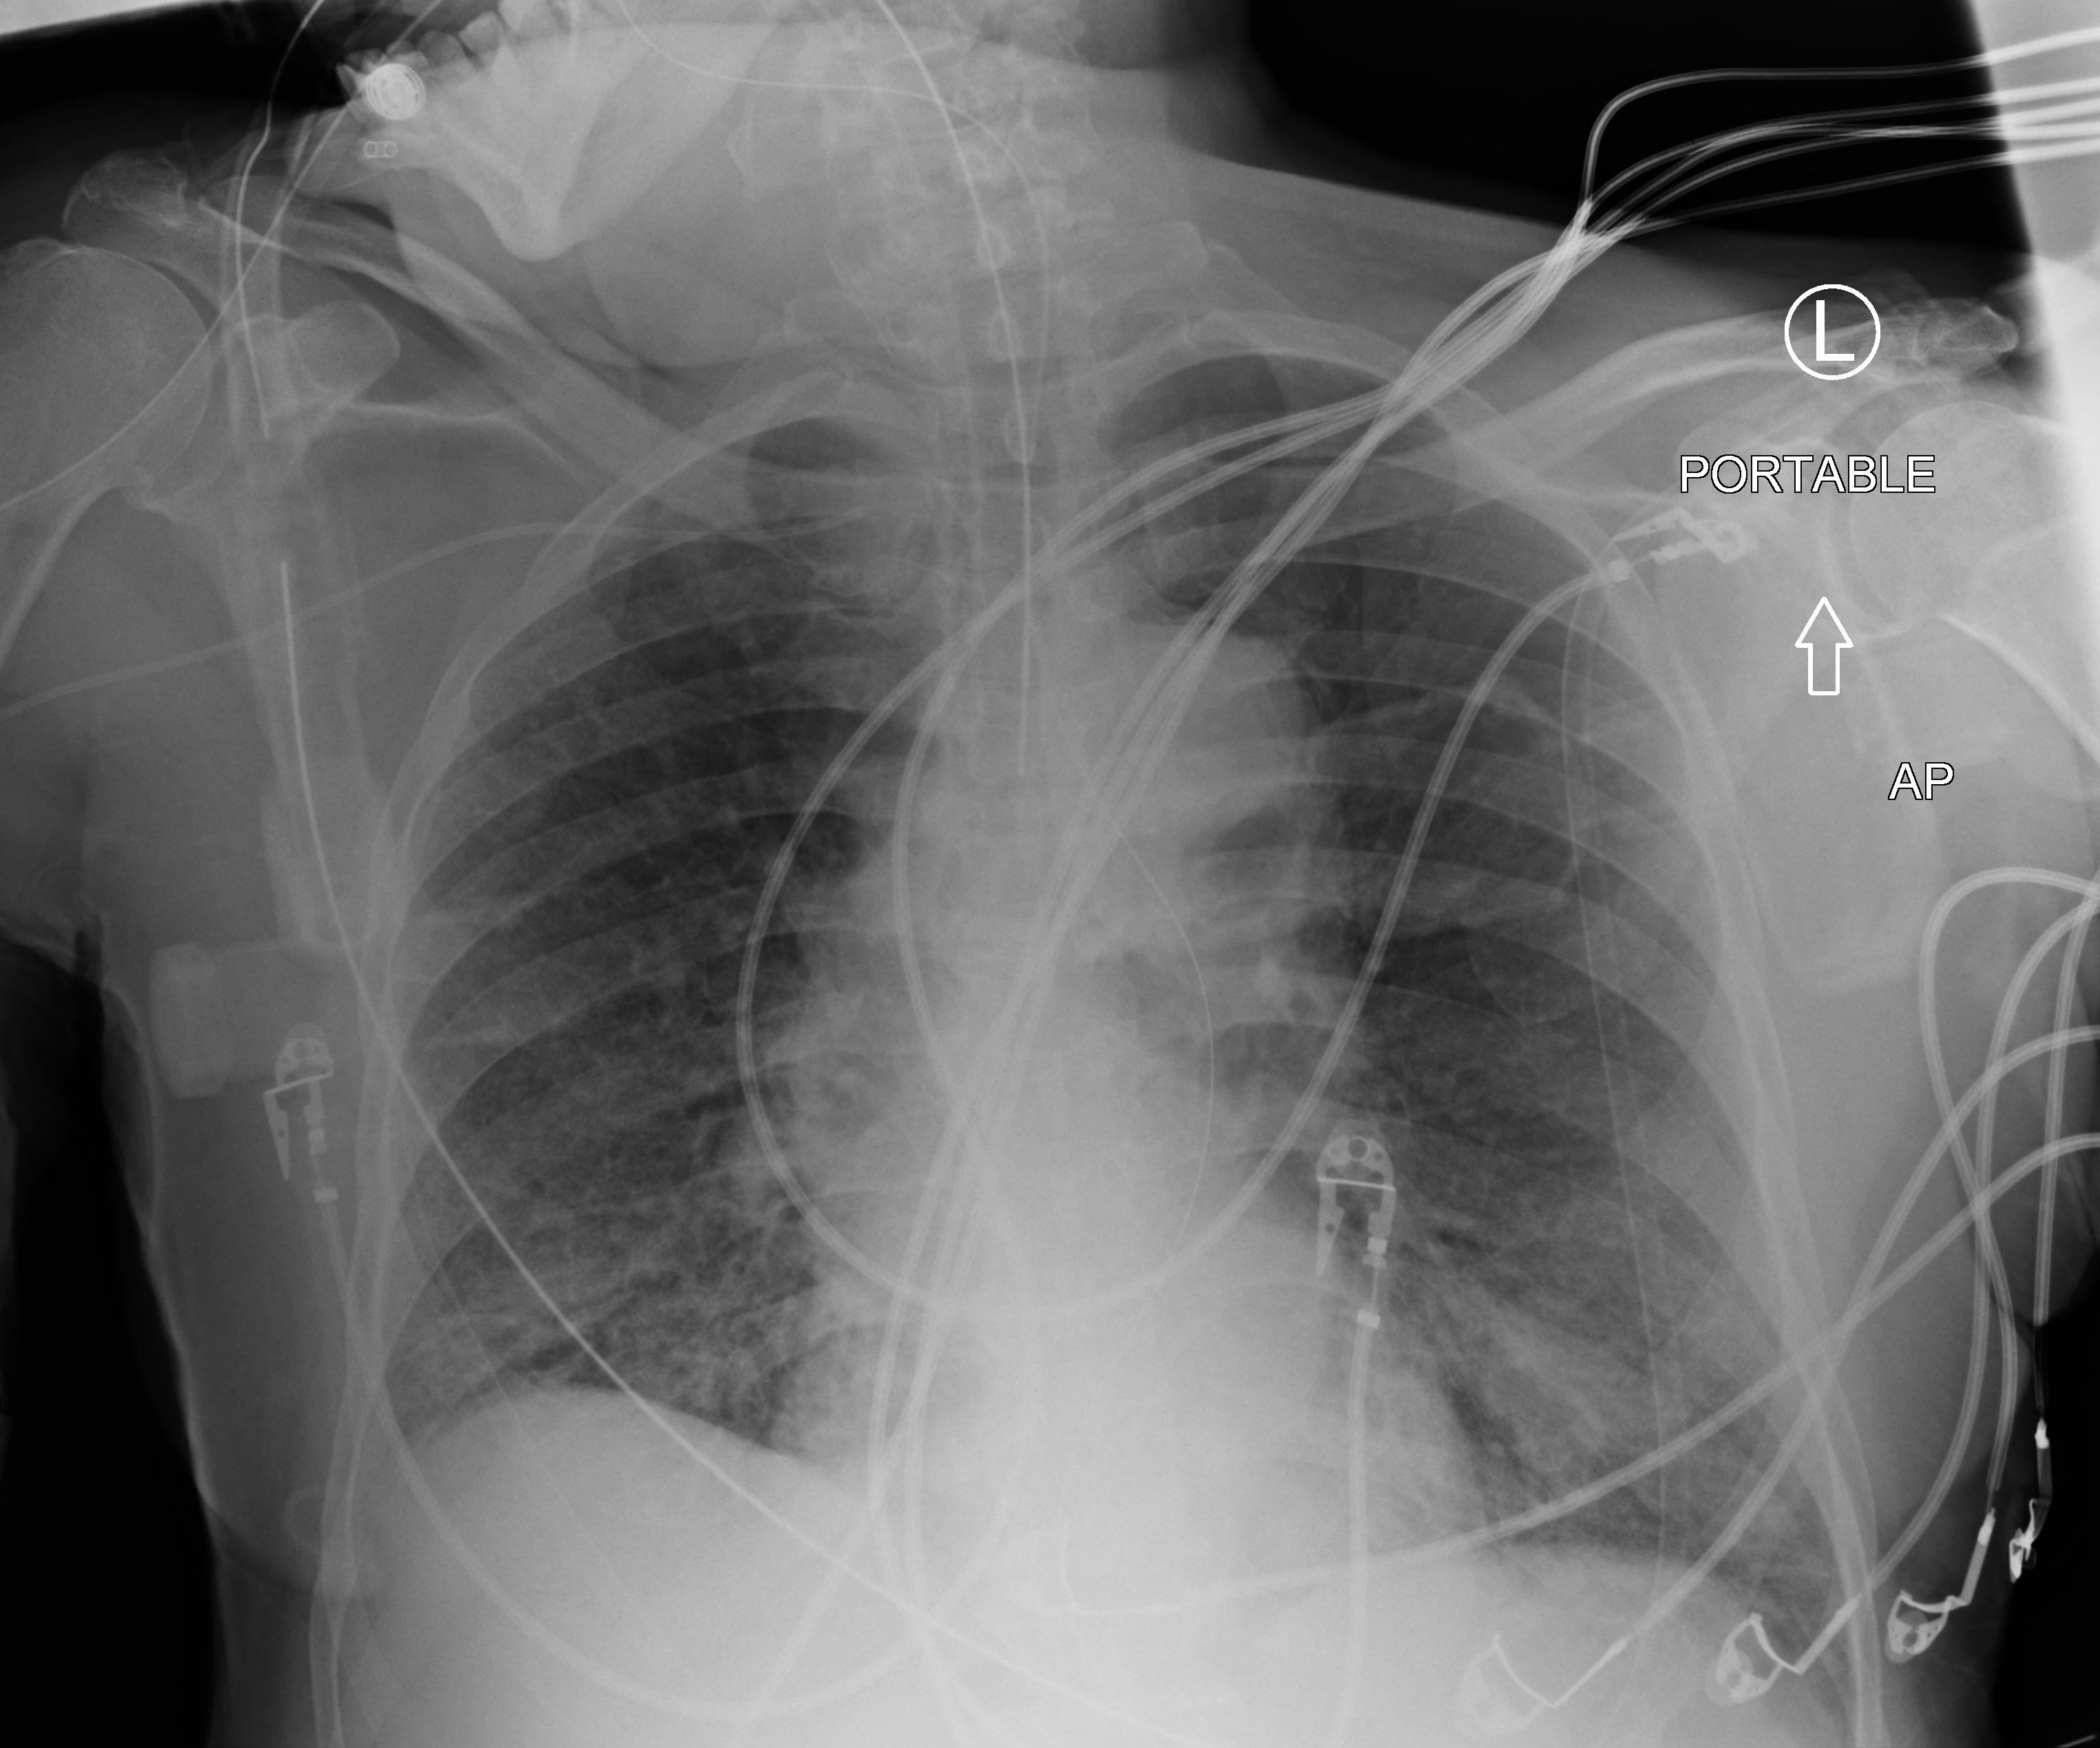
Bedside chest radiograph (computed radiography). Patient hospitalised with COVID-19; male, aged 60–74 years.
From the hospital-stay record, not from the radiograph (when in the stay this image was taken is not recorded):
- mechanically ventilated during this hospital stay: yes
- admitted to intensive care during this hospital stay: yes
- chronic kidney disease (admission record): no